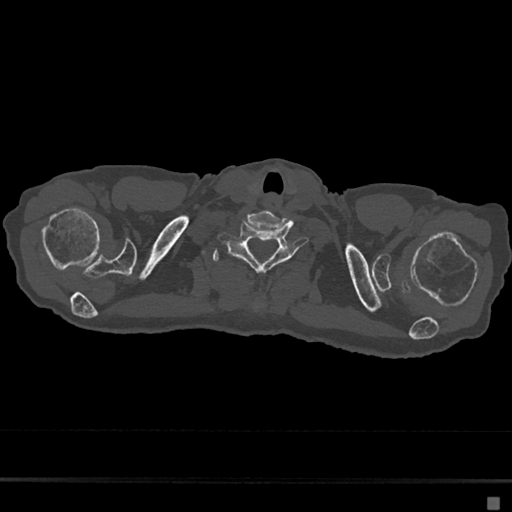
CT including the spine, one axial slice. Position 635 of 797 along the scan axis. Reconstruction kernel Br40s/3. 120 kVp. Bone window (W 1800 / L 400 HU). 512 × 512 image matrix, field of view 360 × 360 mm. Female patient, age 68 years. Case-level facts recorded for this patient, not image findings: primary cancer: renal.
Outlined on this slice (semi-automatically segmented with operator editing):
- T1 vertebra: box from (x=212, y=249) to (x=220, y=263) px